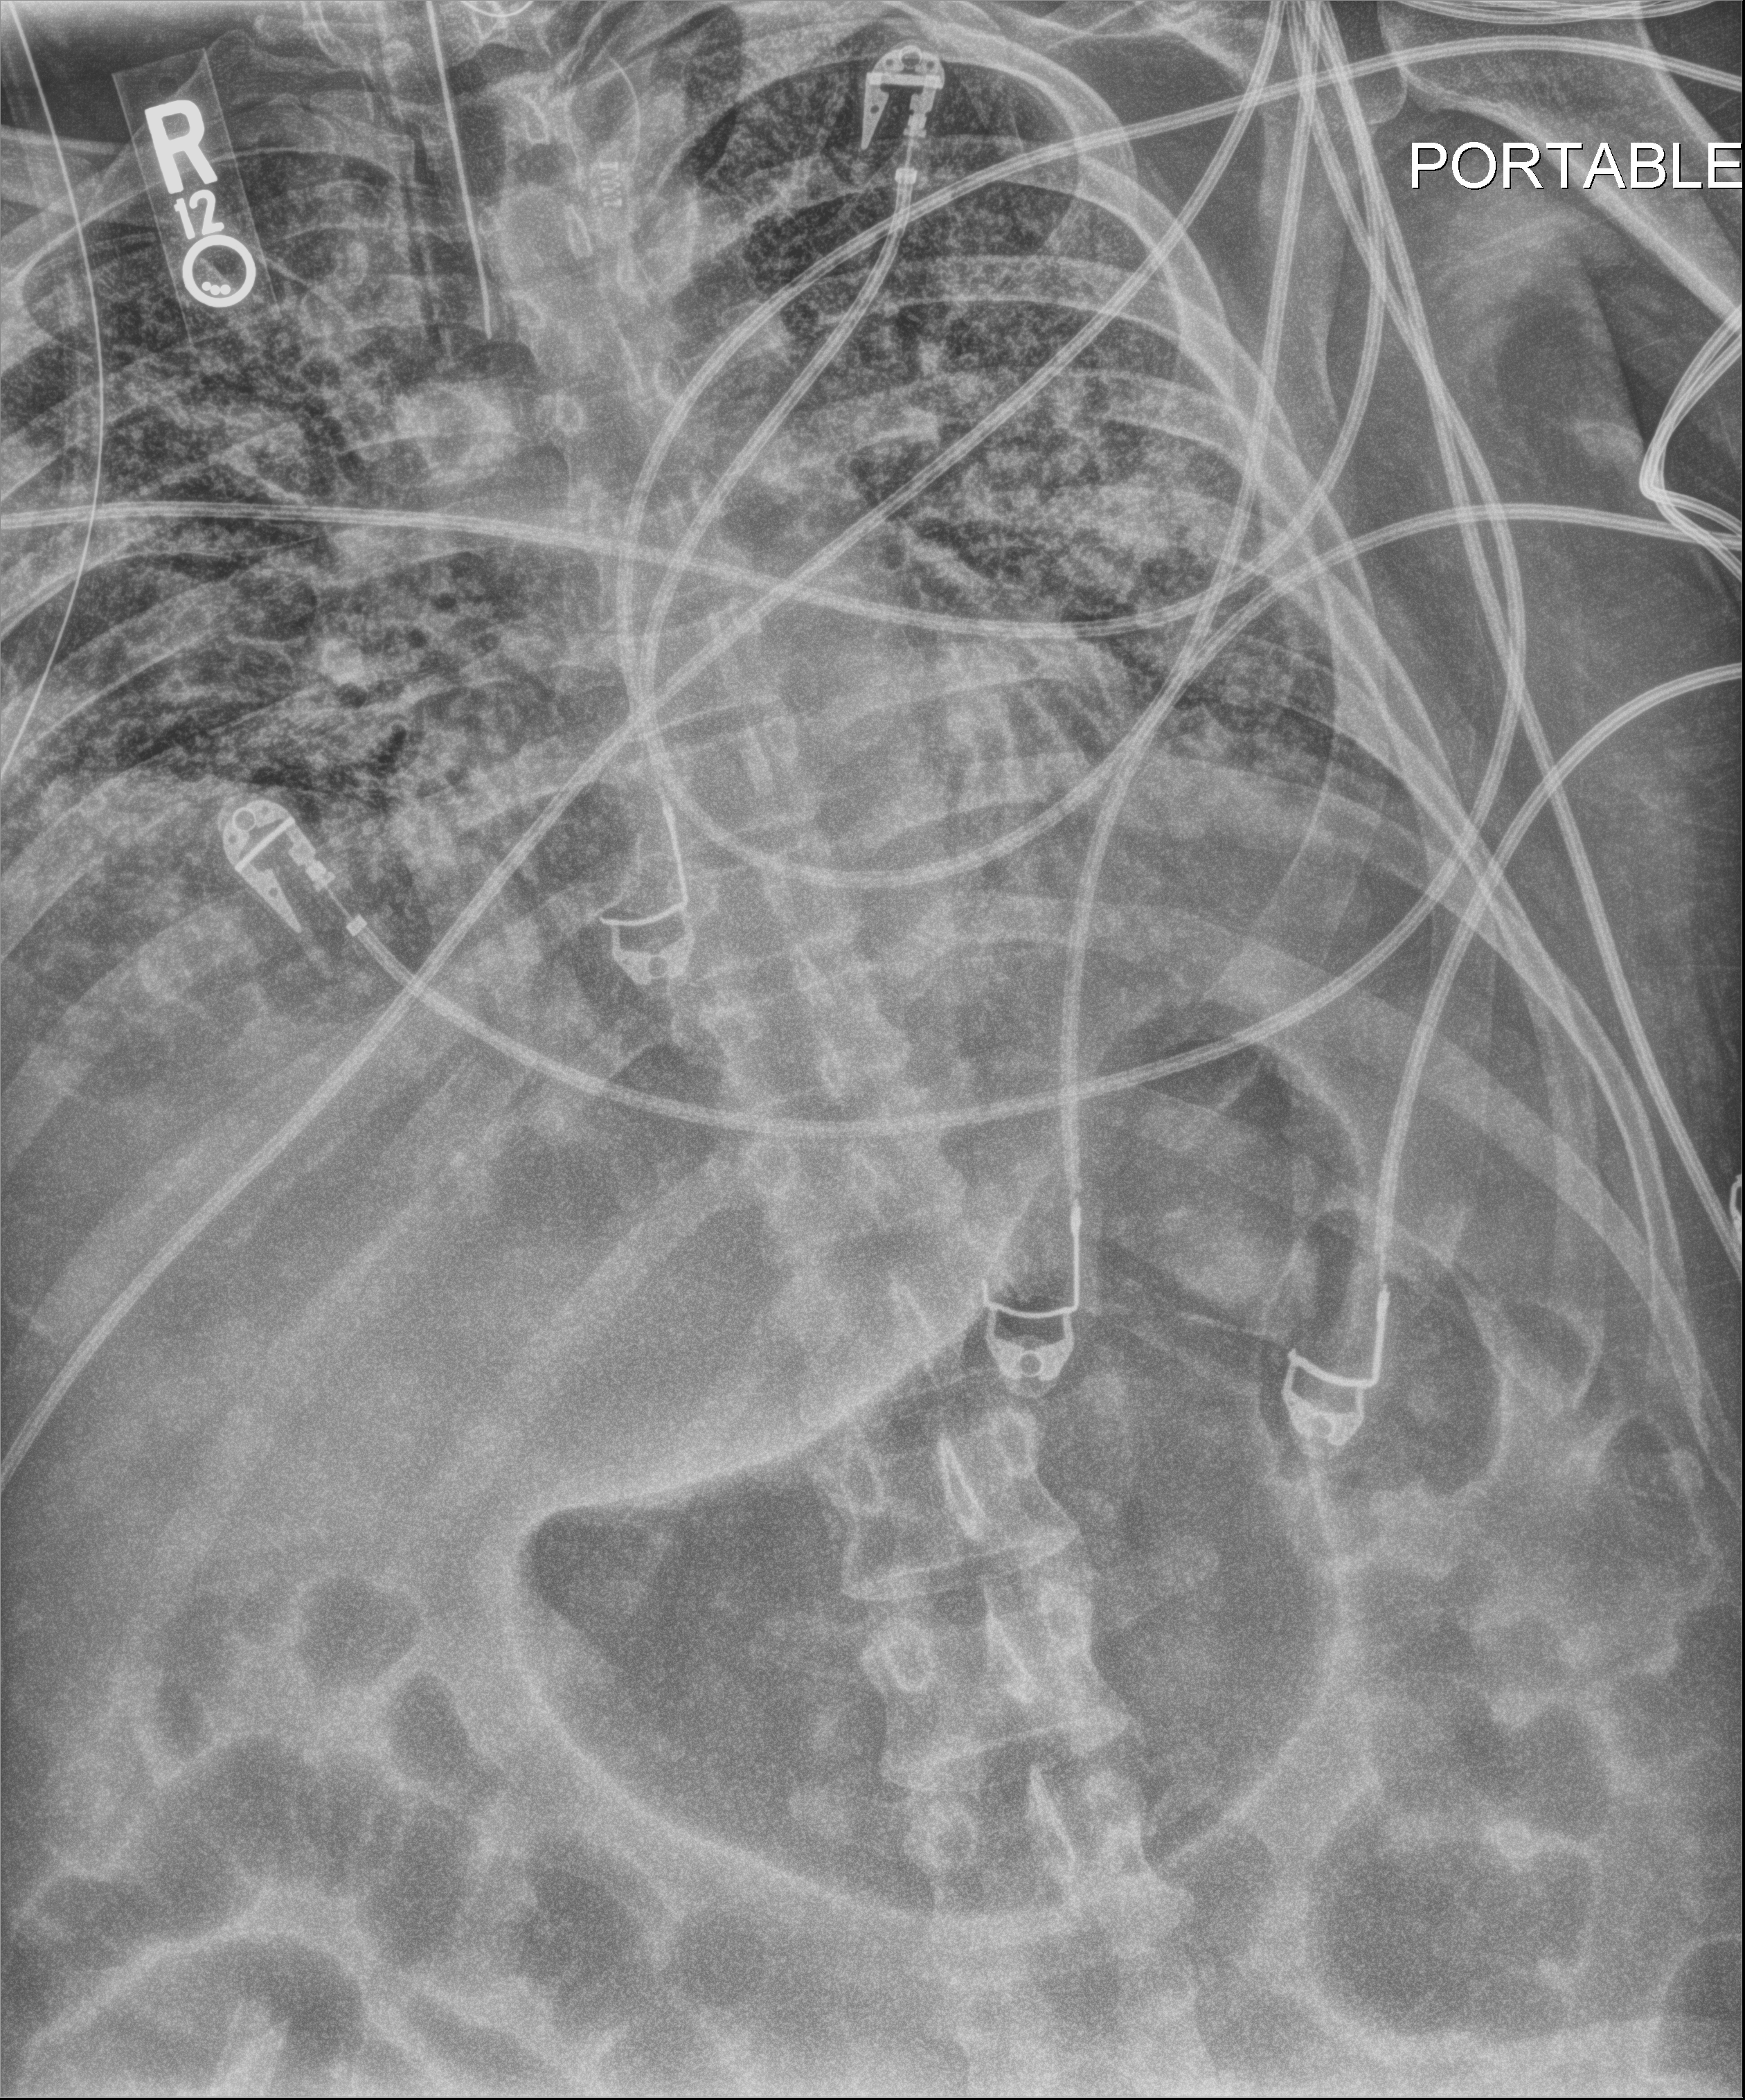
Chest X-ray (portable). Male patient hospitalised with COVID-19, age 18–59 years.
From the hospital-stay record, not from the radiograph (when in the stay this image was taken is not recorded):
- other chronic lung disease (admission record): no
- COPD (admission record): no
- admitted to intensive care during this hospital stay: yes